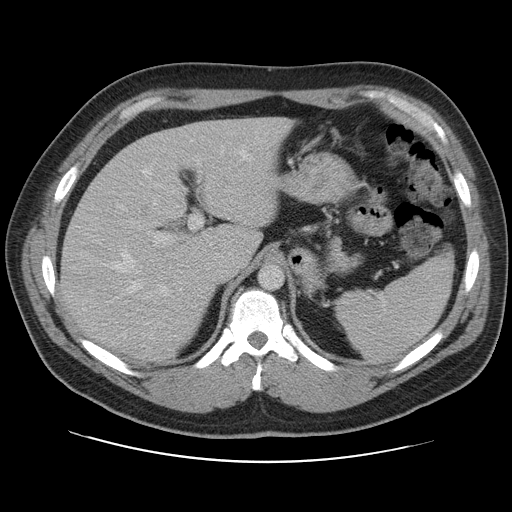
Contrast-enhanced abdominal CT, one axial slice. Slice 77 of 109 in the series (ordered by position). 120 kVp. Intravenous contrast given. Soft-tissue window (W 400 / L 40 HU). 512 × 512 image matrix. Male patient, age 35 years. From the clinical record (not read from this slice): diagnosis: colorectal cancer liver metastases, imaged before liver resection; multiple liver metastases: yes; largest metastasis: 2.8 cm; chemotherapy before resection: yes.
Structures marked on this image (outlined manually by an expert reader):
- hepatic veins: bounding box [x1, y1, x2, y2] px = [103, 149, 252, 324]
- liver: [61, 118, 288, 361]
- planned liver remnant (the part of the liver to remain after resection): [61, 118, 281, 359]
- portal vein (with intrahepatic branches): [92, 160, 203, 299]